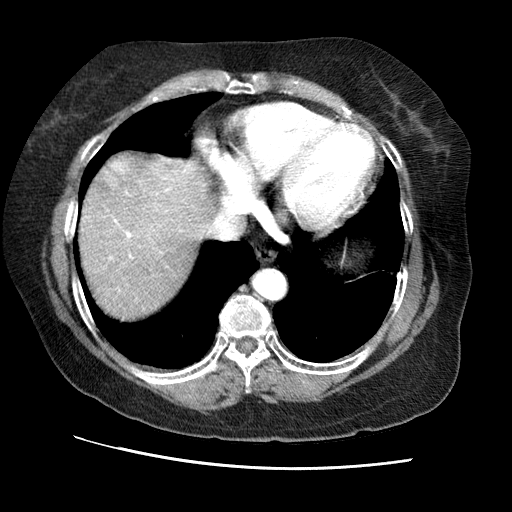
Contrast-enhanced abdominal CT (liver protocol), one axial slice; slice 64 of 65 in the series (ordered by position); 120 kVp; soft-tissue window (W 400 / L 40 HU); 512 × 512 image matrix, field of view 340 × 340 mm. Case-level facts recorded for this patient, not image findings: diagnosis: hepatocellular carcinoma (patient treated with transarterial chemoembolisation; whether this scan precedes or follows treatment is not stated here); TNM stage (as recorded): Stage-II; Child-Pugh class: A; tumour nodularity: multinodular; tumour size: 2.5 cm.
Outlined on this slice (semi-automatically segmented with operator editing):
- liver parenchyma outside the tumour (the mass and vessels are separate outlines, so this box may not span the whole liver): bounding box <80,154,216,318> (left, top, right, bottom; pixels)
- mass: <98,155,133,191>
- liver vessels: <109,160,190,260>